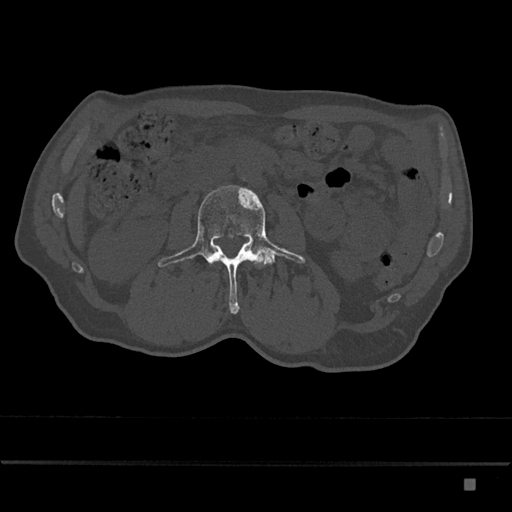
CT including the spine, one axial slice. Position 412 of 797 along the scan axis. Reconstruction kernel Br40s/3. 120 kVp. Bone window (W 1800 / L 400 HU). 0.5 mm slice thickness. 512 × 512 image matrix, field of view 390 × 390 mm. Male patient, age 72 years. Case-level facts recorded for this patient, not image findings: primary cancer: prostate.
Structures marked on this image (semi-automatic segmentation, software-assisted and operator-edited):
- L3 vertebra: bounding box (x1, y1, x2, y2) in pixels: (158, 185, 306, 314)